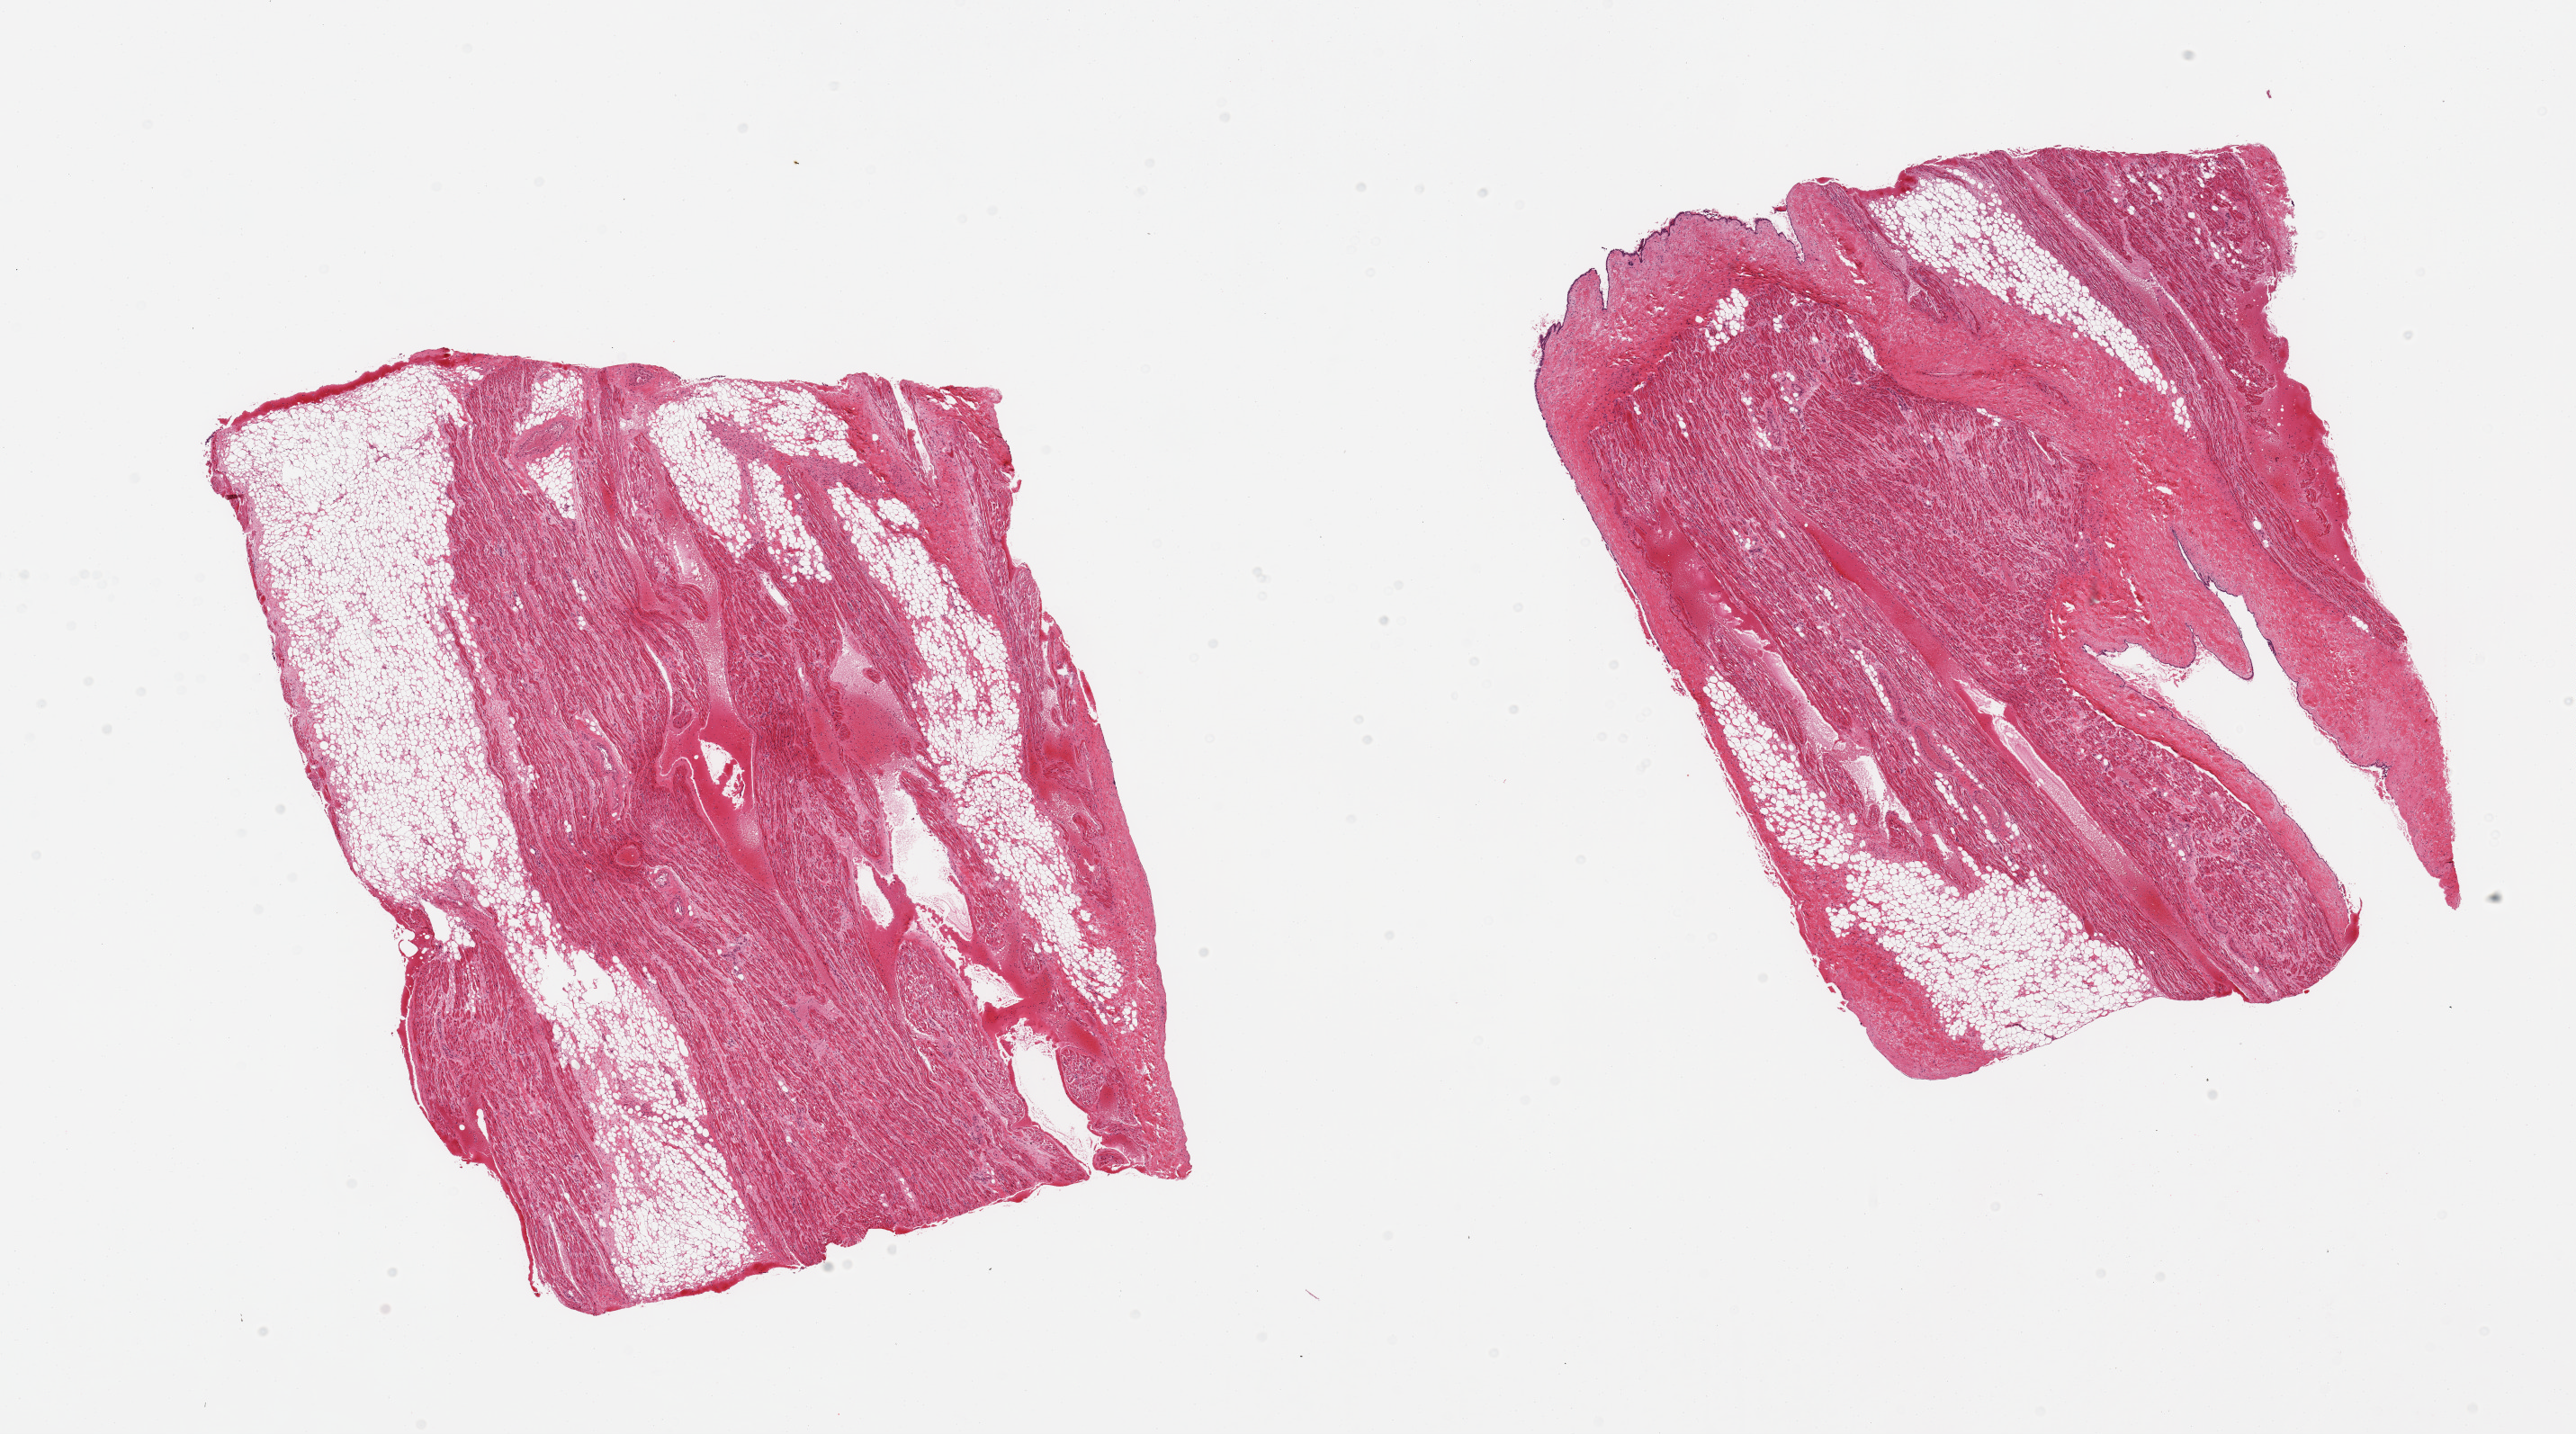
Digitized H&E-stained section, whole scanned area (about 22.6 x 12.6 mm) shown as a low-resolution overview, PAXgene-fixed, paraffin-embedded tissue, section of auricular appendage (target tissue), donor tissue sample. Donor sex: male.
Reviewer comment on this tissue sample: 2 pieces, no significant abnormalities.